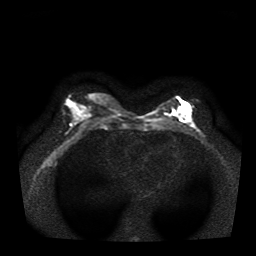
Breast MRI, one axial slice; position 16 of 35 along the scan axis; diffusion-weighted series; image 2 of 4 stored at this slice position (different b-values; order by instance number); 1.5 T; 5 mm slice thickness; 256 × 256 image matrix, field of view 330 × 330 mm. Female patient.
Outlined on this slice (expert manual segmentation):
- tumour on diffusion-weighted imaging: box from (x=176, y=110) to (x=183, y=116) px